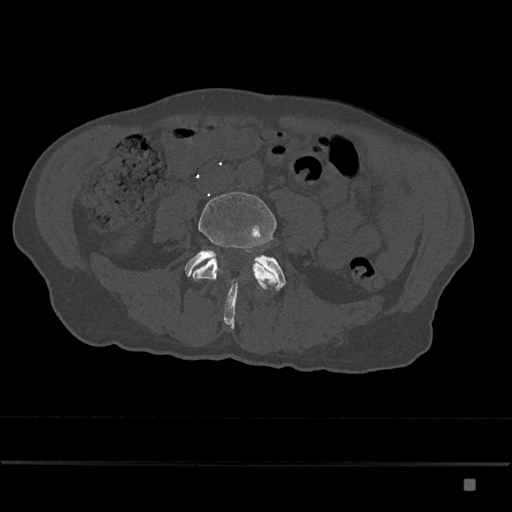
CT including the spine, one axial slice; slice 315 of 797 in the series (ordered by position); reconstruction kernel Br40s/3; bone window (W 1800 / L 400 HU); 0.5 mm slice thickness; 512 × 512 image matrix, field of view 390 × 390 mm. Patient: male, 72 years. Case-level facts recorded for this patient, not image findings: primary cancer: prostate.
Structures marked on this image (semi-automatic segmentation, software-assisted and operator-edited):
- L4 vertebra: box from (x=190, y=192) to (x=277, y=289) px
- L5 vertebra: (x=185, y=250)–(x=286, y=329)